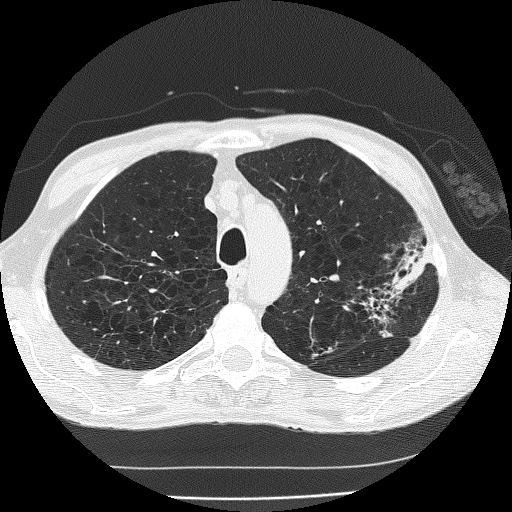
Low-dose screening chest CT, one axial slice. Slice 143 of 185 in the series (ordered by position). Reconstruction kernel FC51. Lung window (W 1500 / L -600 HU). 2 mm slice thickness. 512 × 512 image matrix, field of view 320 × 320 mm.
Structures marked on this image (outlined manually by an expert reader):
- lesion 1 (tumor, upper lobe of left lung): bounding box (x1, y1, x2, y2) in pixels: (387, 254, 426, 298)